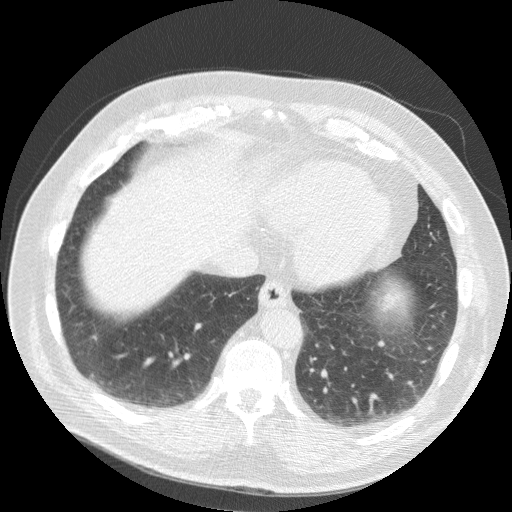
Chest CT (low-dose screening protocol), one axial image, second screening round (one year after baseline), lung window (W 1500 / L -600 HU), 2.5 mm slice thickness, standard (soft-tissue) reconstruction kernel (STANDARD), slice 68 of 188 in the series. Male, age 63 years at enrolment.
Expert reader's lesion annotation, bounding box [x1, y1, x2, y2] px = [362, 281, 410, 323]. The screening reader recorded 2 non-calcified nodules or masses ≥4 mm on this exam (right middle lobe, left lower lobe); which of them this box marks is not recorded.